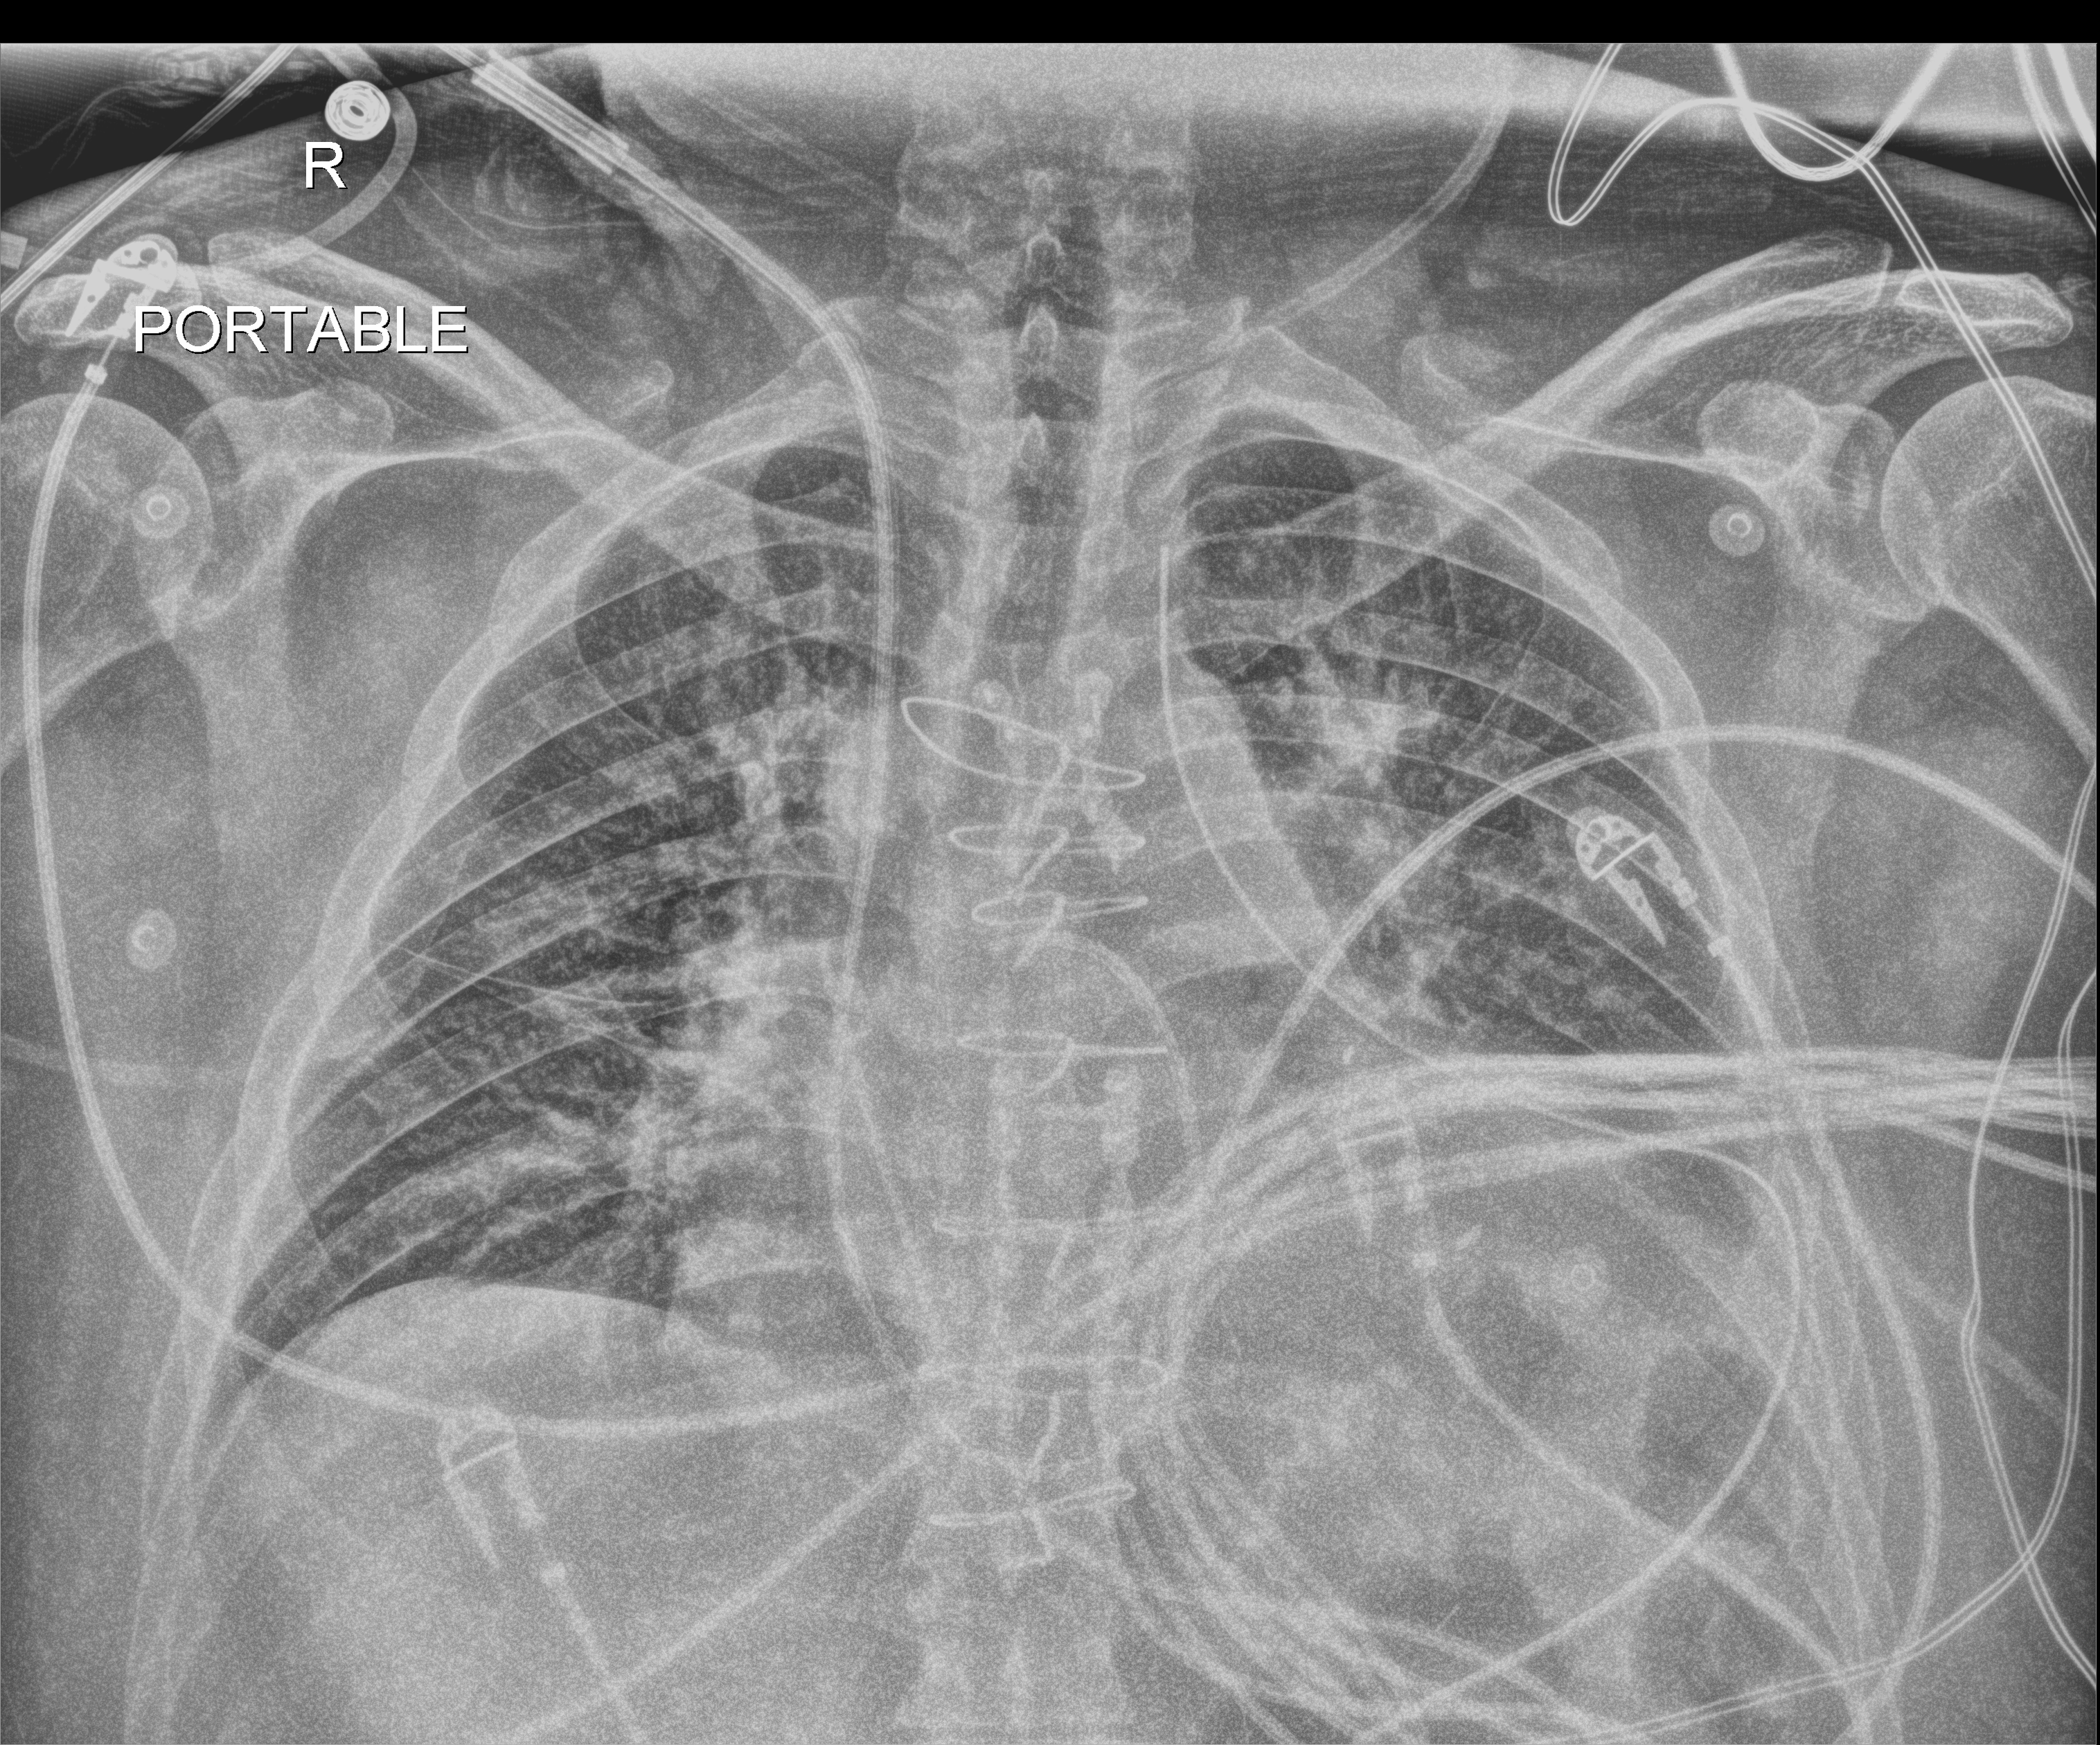
Portable chest radiograph, anteroposterior (AP) projection. Male patient hospitalised with COVID-19, age 18–59 years.
Hospital-stay facts (about this admission, not read from this image; timing relative to this image not recorded): mechanically ventilated during this hospital stay: no.